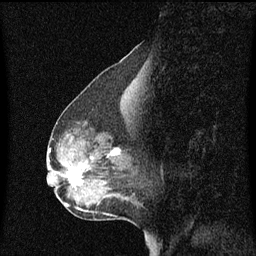
Breast MRI (dynamic contrast-enhanced), one sagittal slice; position 26 of 60 along the scan axis; dynamic contrast-enhanced series, image 2 of 3 at this slice position (ordered by acquisition); 1.5 T; TE 4.2 ms, TR 8.4 ms; 2 mm slice thickness; 256 × 256 image matrix, field of view 200 × 200 mm. Female patient, age 50 years. From the clinical record (not read from this slice): setting: breast cancer imaged before/during neoadjuvant chemotherapy; receptor status: HR-positive, HER2-negative.
Outlined on this slice (semi-automatic segmentation, software-assisted and operator-edited):
- analysis volume of interest (the breast-tissue region the enhancement analysis was run in; not a lesion): bounding box (x1, y1, x2, y2) in pixels: (61, 144, 129, 189)
- tumour enhancement mask (voxels above the 70 % enhancement threshold inside the analysis volume of interest): (69, 150, 121, 185)